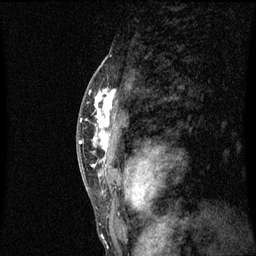
Breast MRI (dynamic contrast-enhanced), one sagittal slice; slice 40 of 60 in the series (ordered by position); dynamic contrast-enhanced series, image 2 of 3 at this slice position (ordered by acquisition); 1.5 T; TE 4.2 ms, TR 8.9 ms; 2 mm slice thickness; 256 × 256 image matrix. Female patient, age 50 years. From the clinical record (not read from this slice): setting: breast cancer imaged before/during neoadjuvant chemotherapy; receptor status: triple-negative.
Structures marked on this image (semi-automatic segmentation, software-assisted and operator-edited):
- analysis volume of interest (the breast-tissue region the enhancement analysis was run in; not a lesion): bounding box <84,80,125,171> (left, top, right, bottom; pixels)
- tumour enhancement mask (voxels above the 70 % enhancement threshold inside the analysis volume of interest): <92,90,117,167>